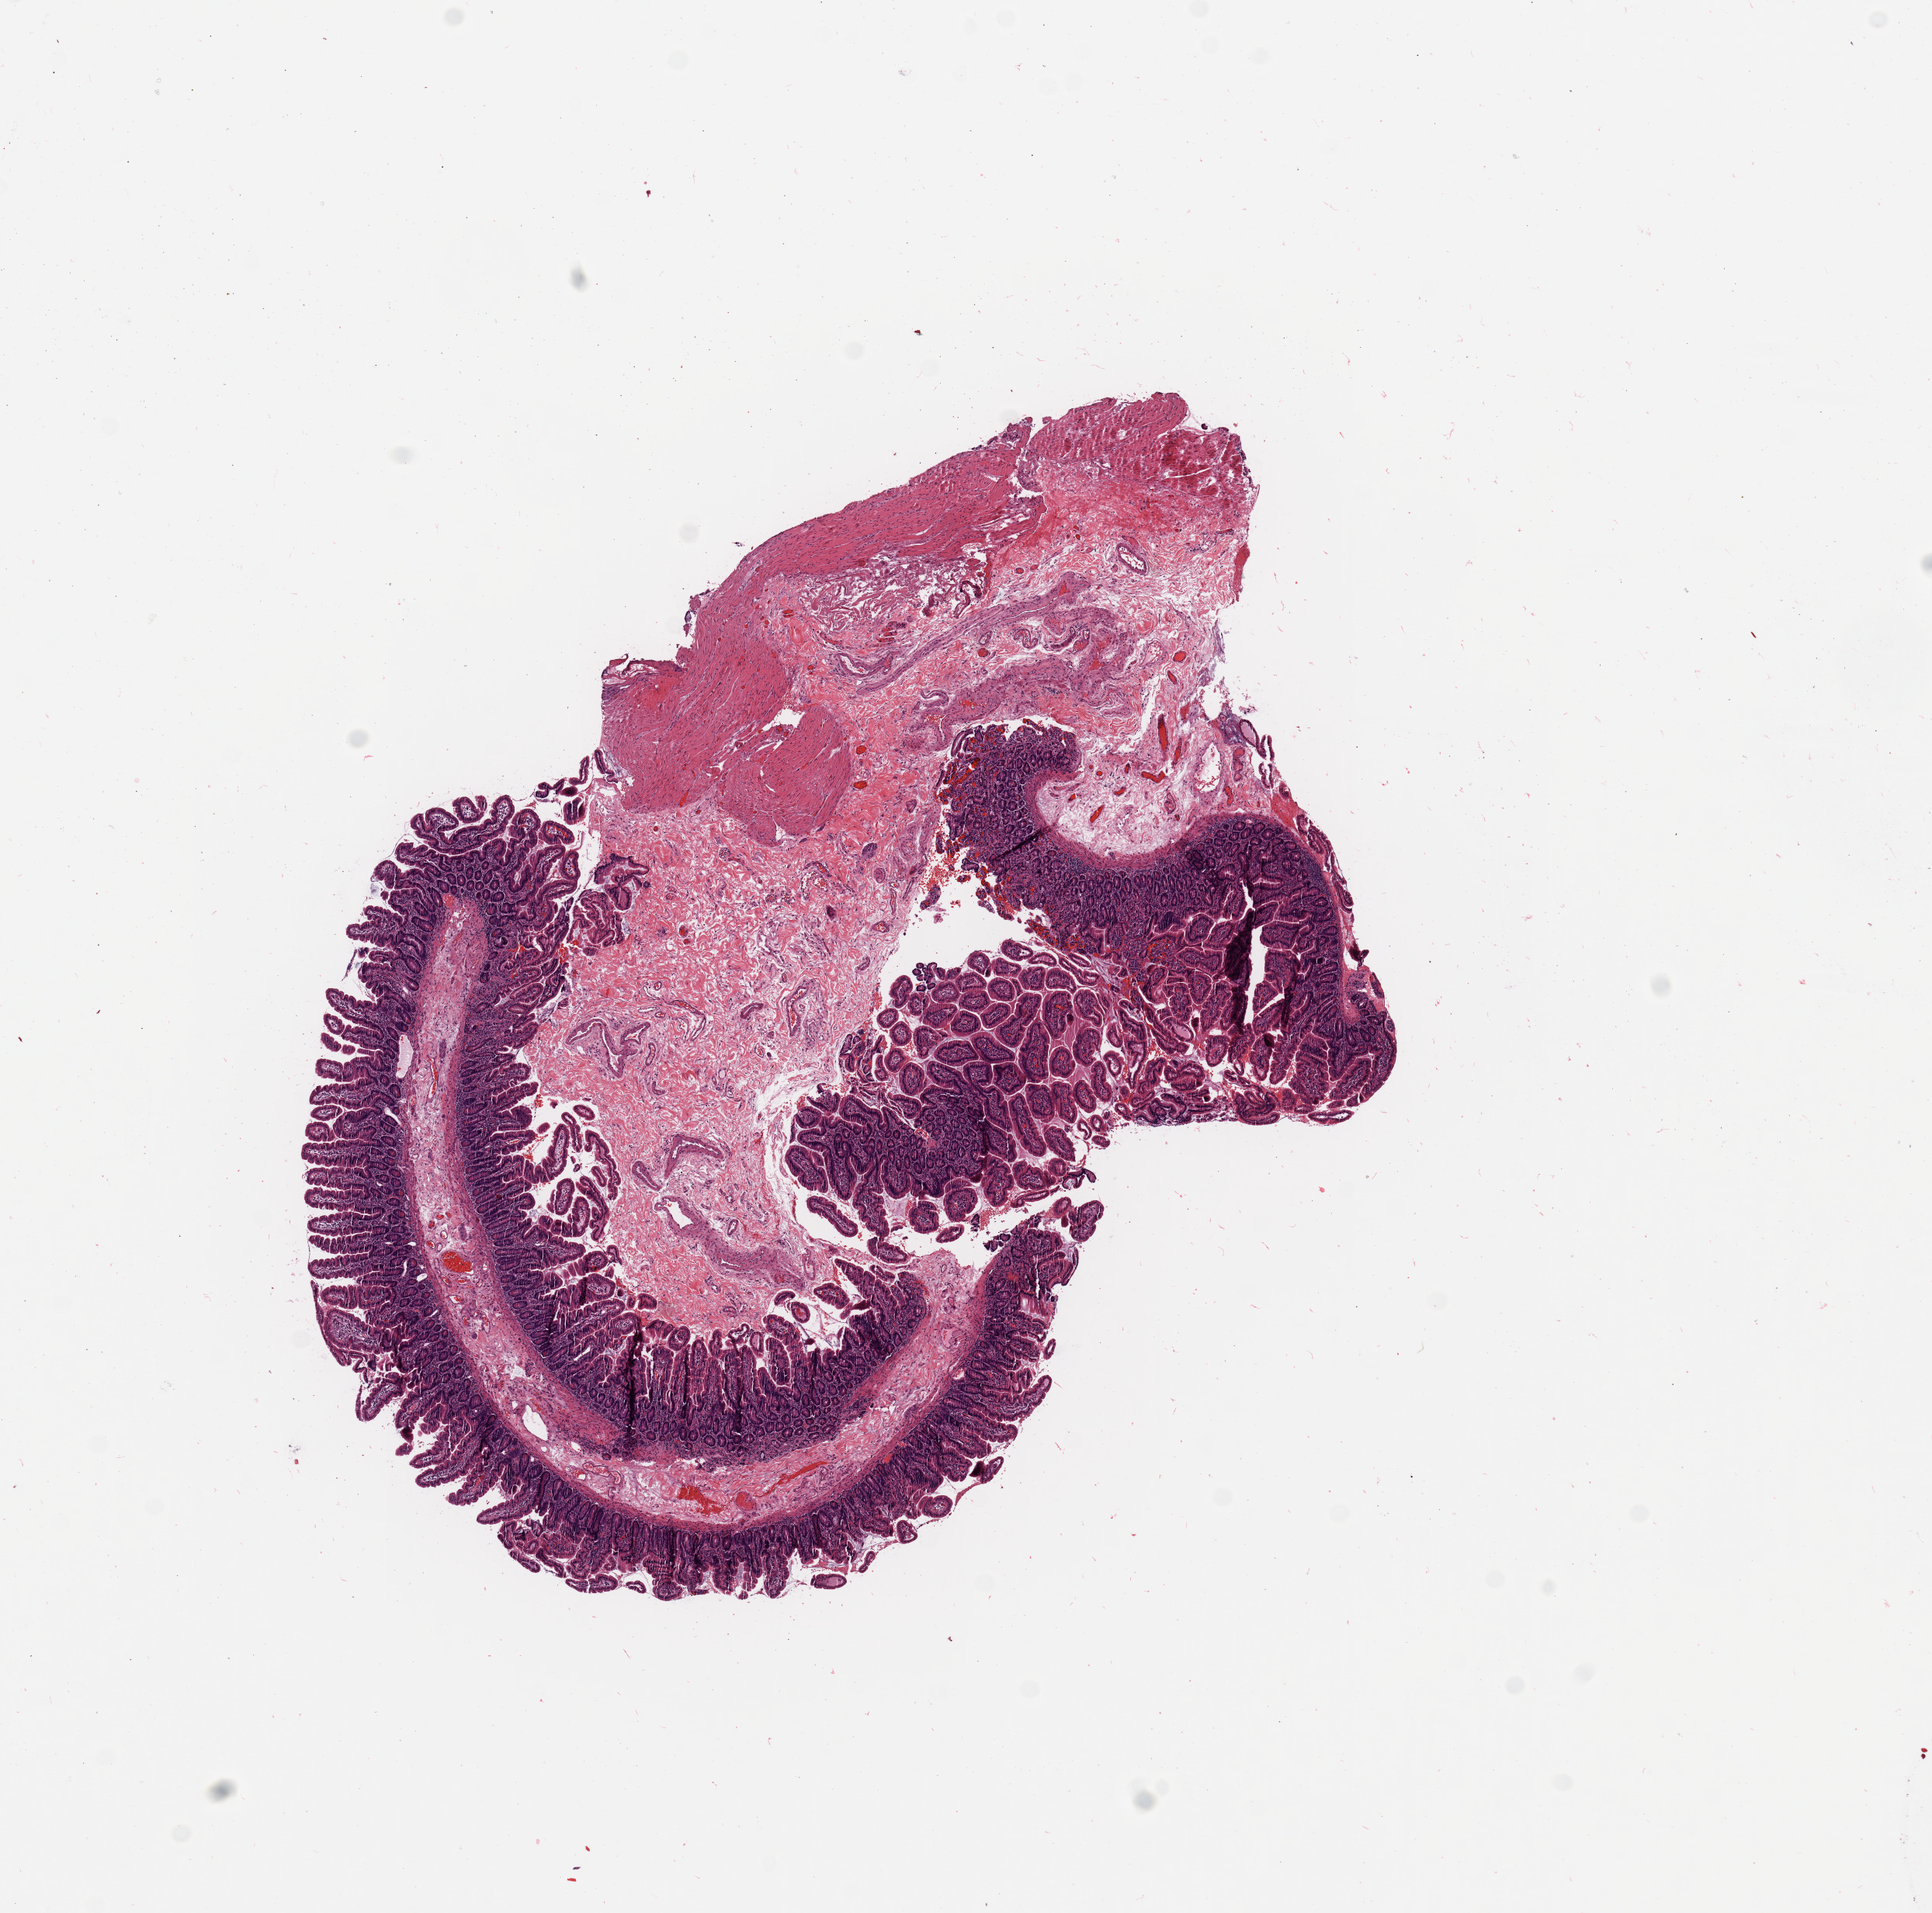
Whole-slide histology image, H&E, whole scanned area (about 9.8 x 9.7 mm) shown as a low-resolution overview, normal (non-tumour) tissue sample, sampled site: pancreas. Male, 63 y/o.
This section: normal (non-tumour) tissue from the same patient. Patient diagnosis: Infiltrating duct carcinoma, NOS.